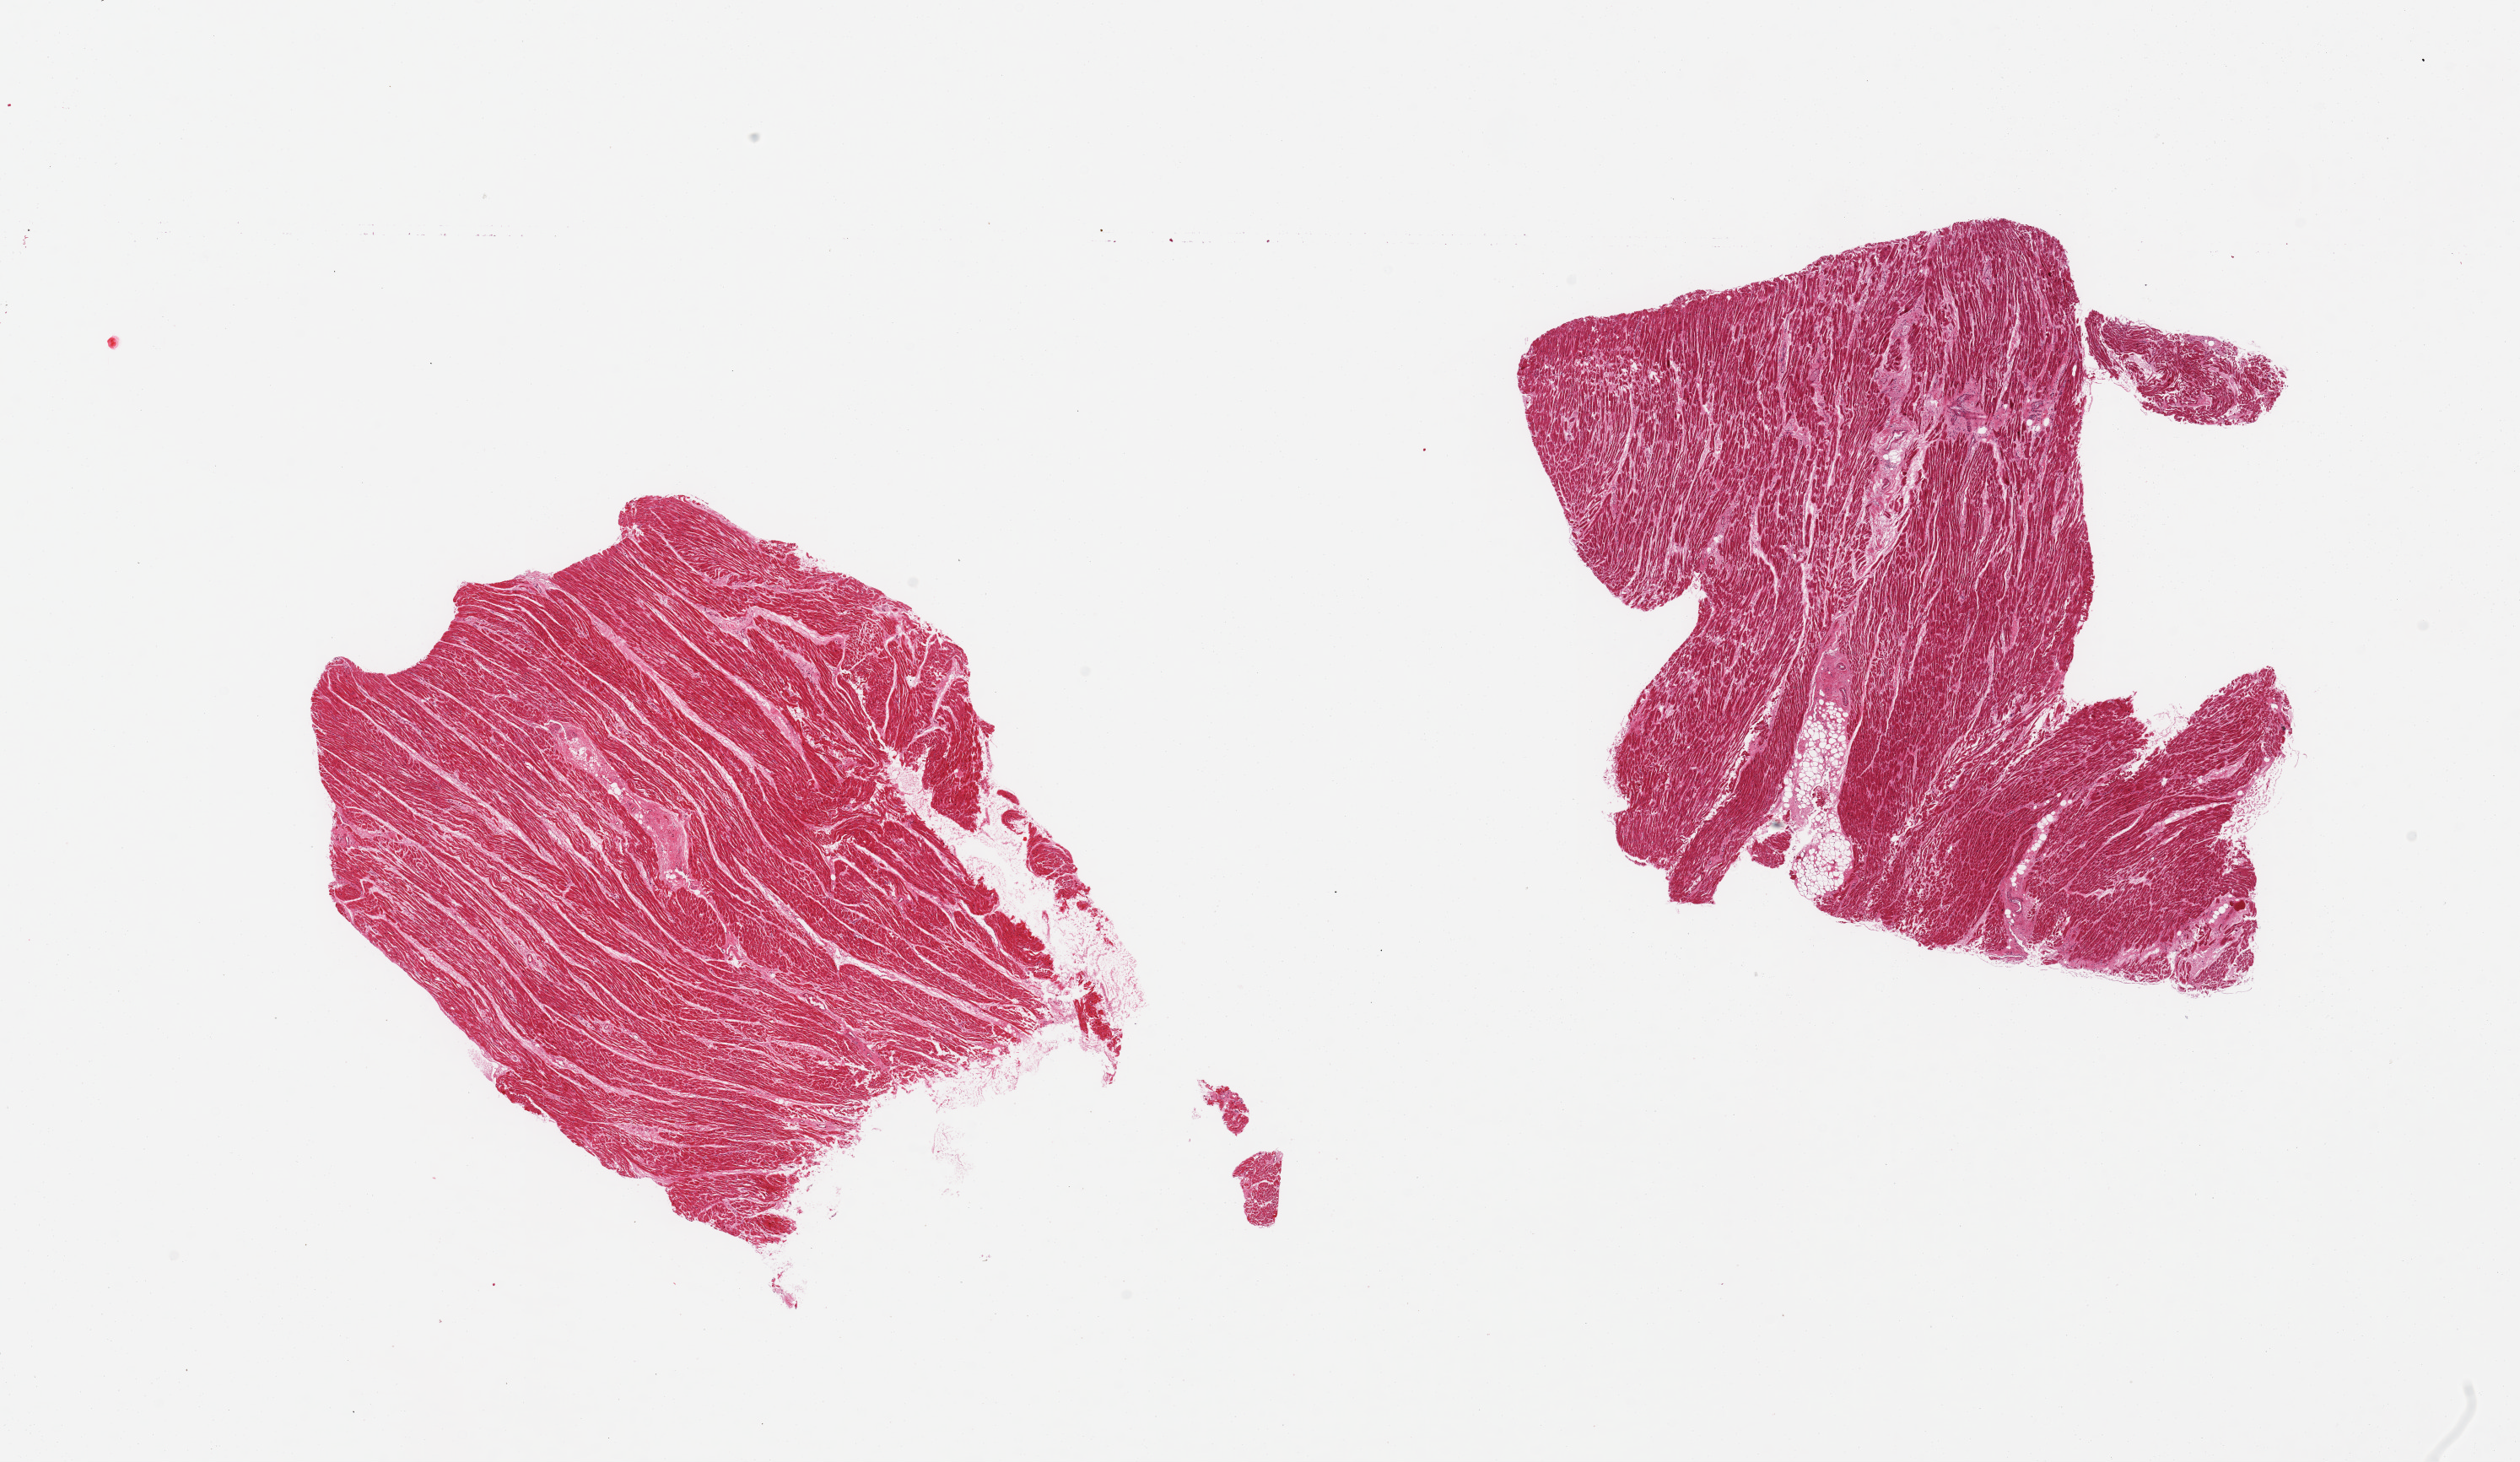
Digitized hematoxylin and eosin (H&E)-stained section — whole scanned area (about 23.6 x 13.7 mm, slide scanned at 20x) shown as a low-resolution overview; PAXgene-fixed paraffin-embedded (PFPE) section; sampled site (target tissue): heart; tissue donor sample. Donor: male.
Reviewer comment on this tissue sample: 2 pieces, pronounced interstitial fibrosis/chronic ischemic changes.